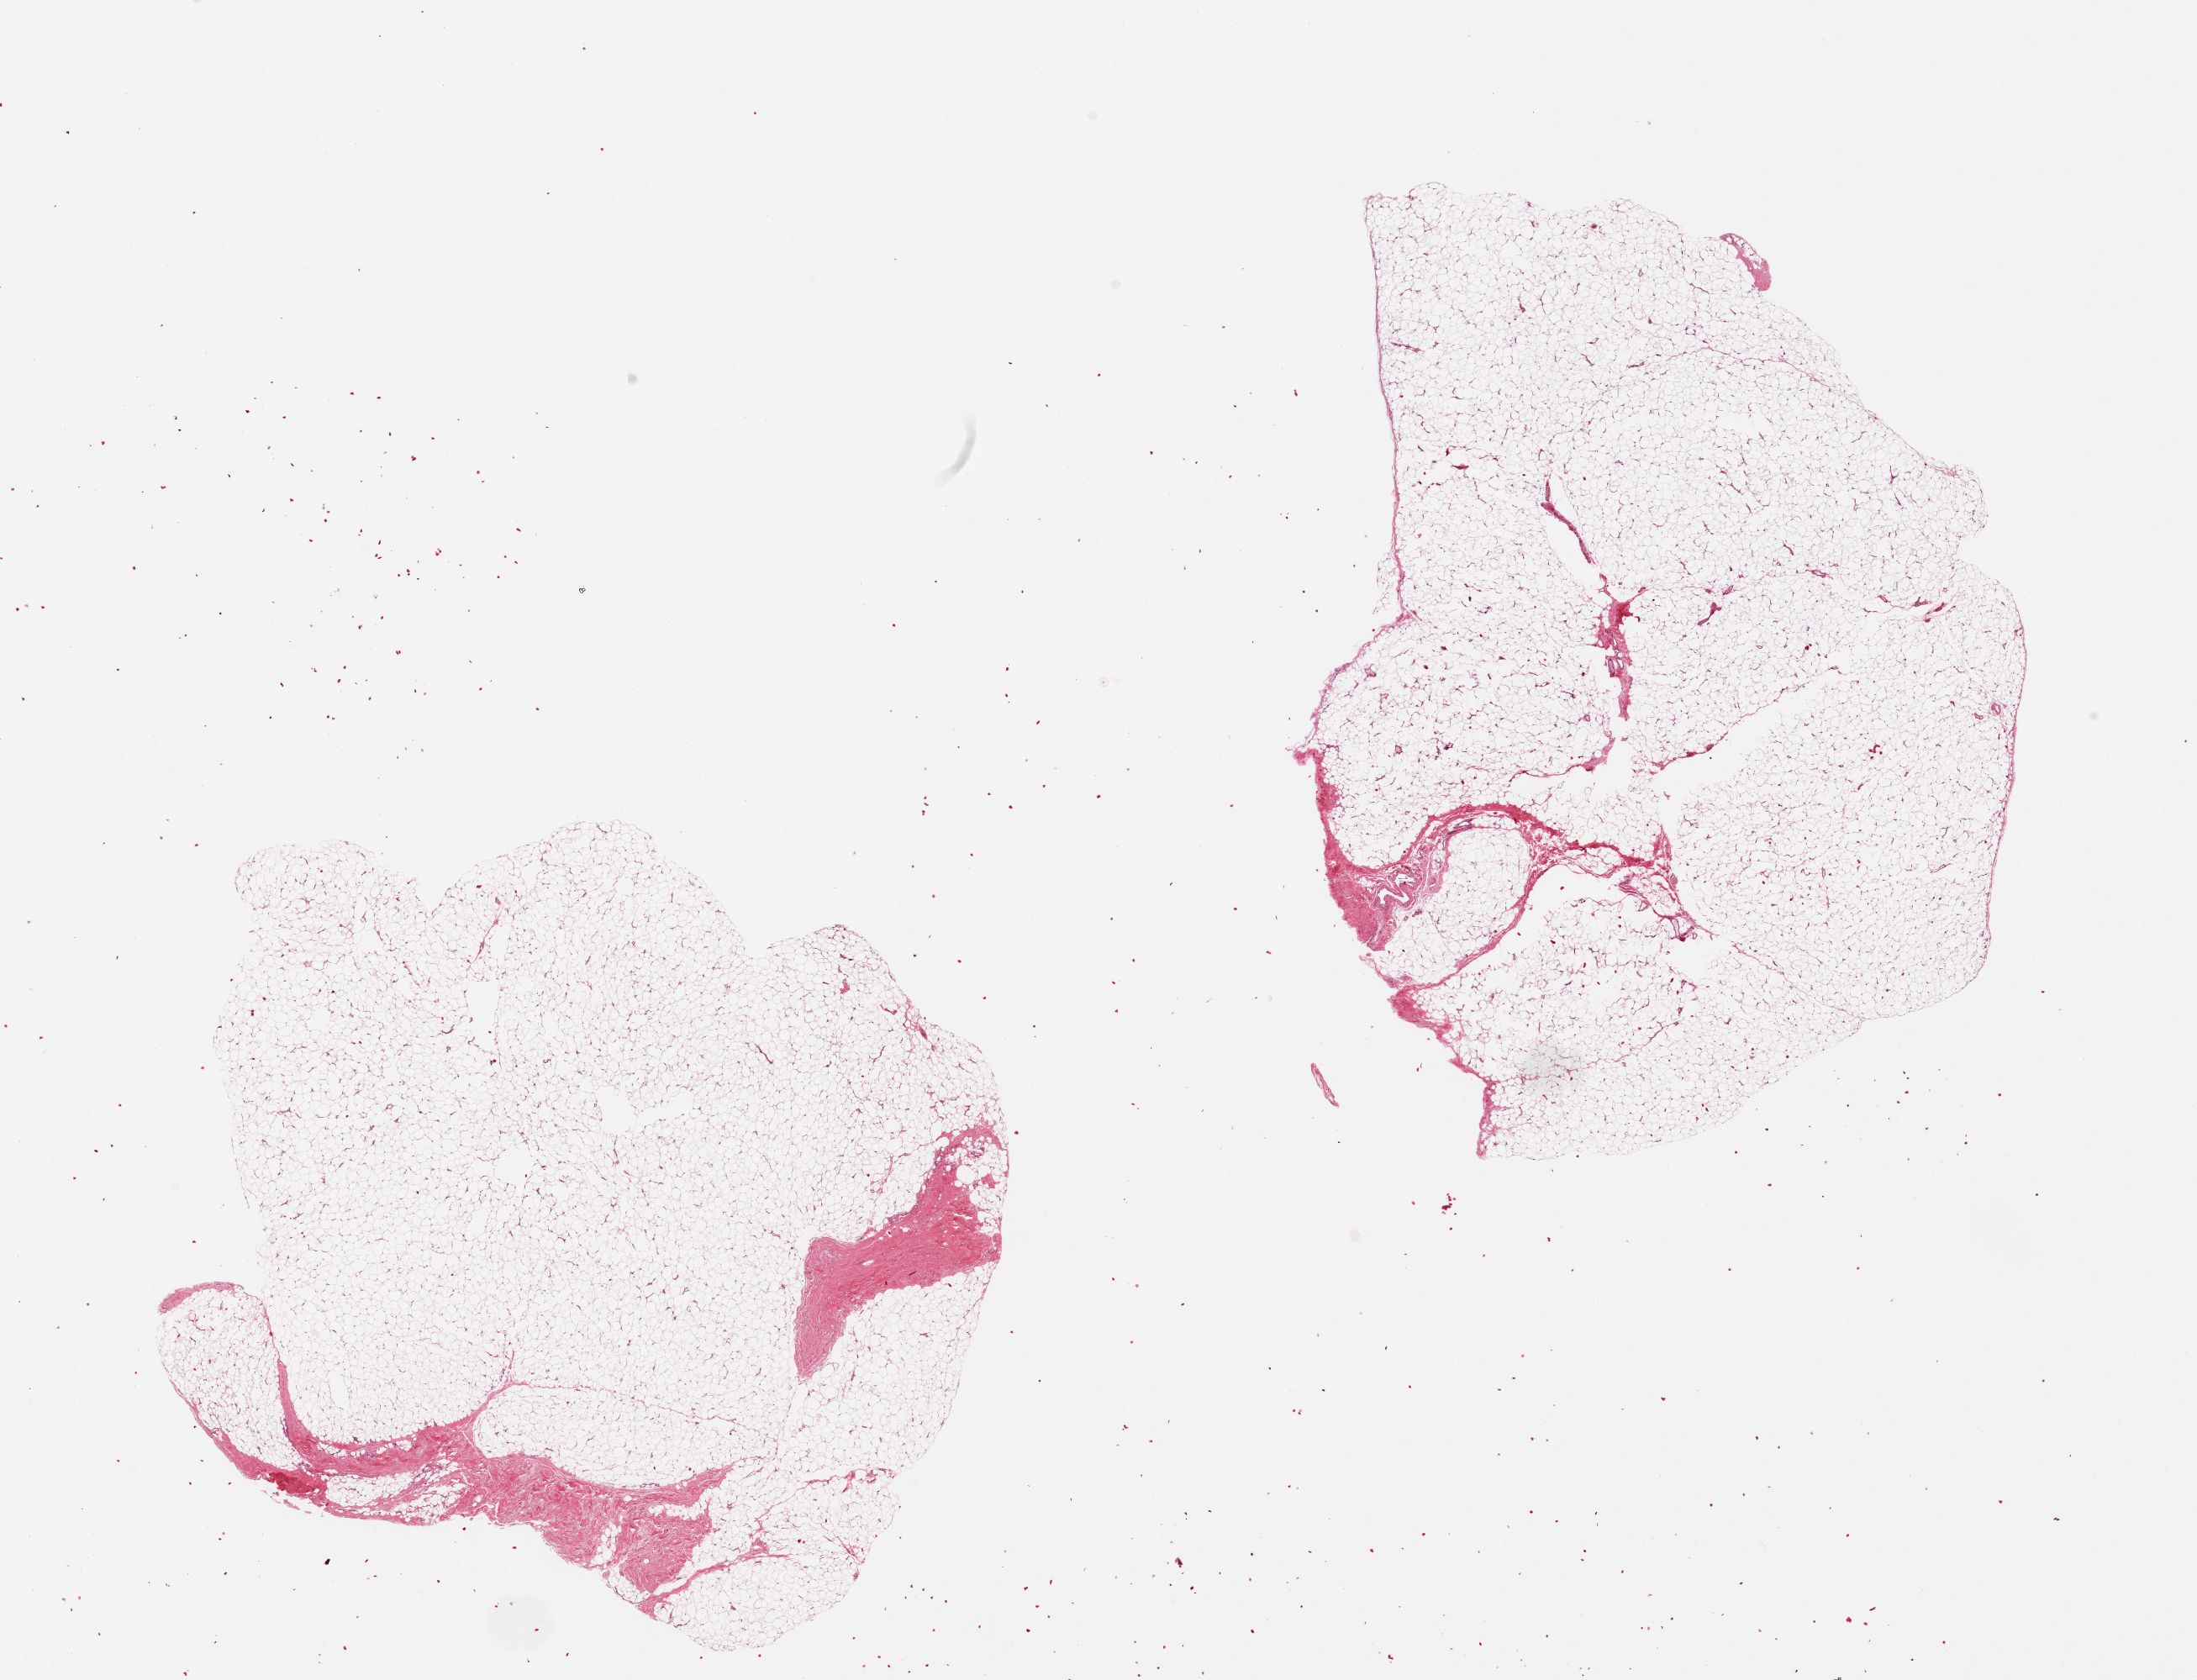
Whole-slide image, hematoxylin and eosin (H&E) stain, brightfield, low-resolution overview of the scanned area, about 20.7 x 15.8 mm (acquisition: 20x scan), PAXgene-fixed, paraffin-embedded tissue, target tissue: adipose tissue, tissue donor sample.
Pathologist's review note for this sample: 2 pieces ~8x7mm.